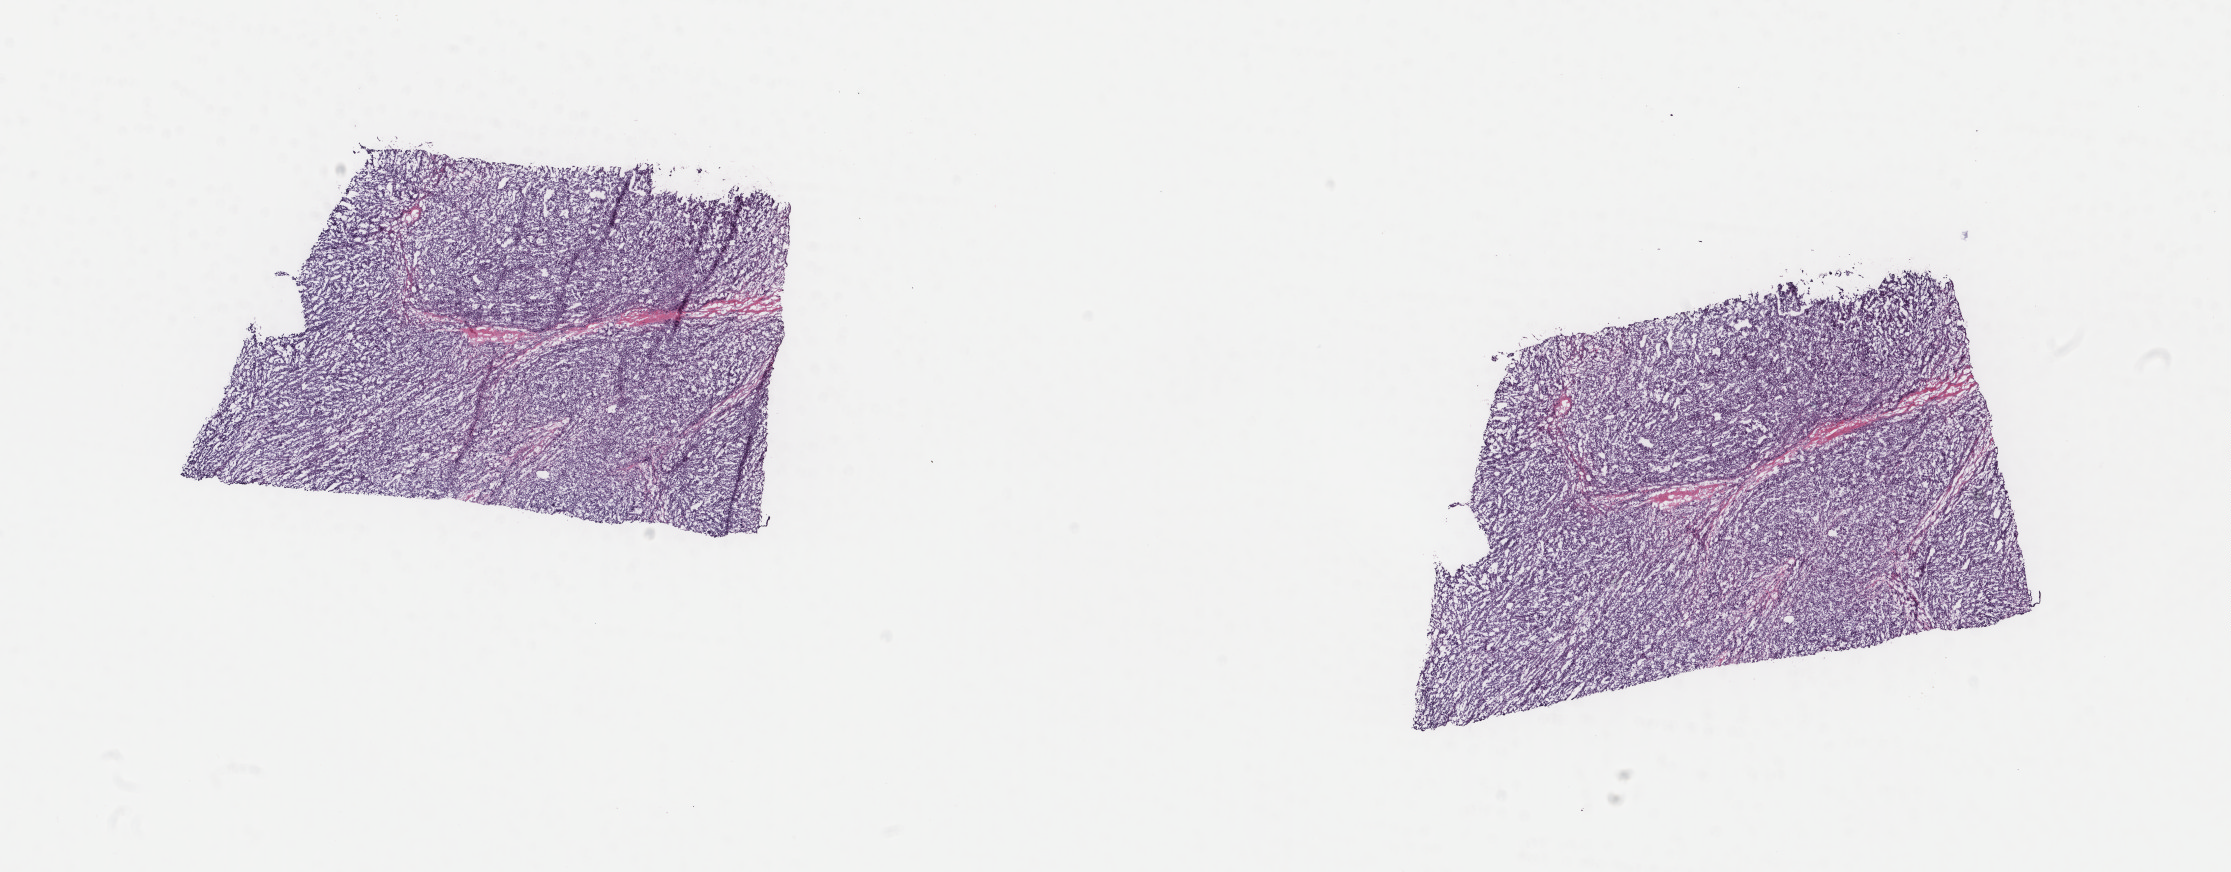
Whole-slide histology image, H&E-stained, a low-resolution overview of the entire scanned area, about 17.7 x 6.9 mm; frozen section; metastatic tumour sample, sampled site not recorded. Male patient; age at initial diagnosis 54 years. Pathologist review of this section (percent, as recorded): tumour cells 100%, tumour nuclei 97%, normal cells 0%, stromal cells 0%, necrosis 0%. Inflammatory infiltration, as recorded: lymphocyte infiltration 0%, monocyte infiltration 0%, neutrophil infiltration 0%.
• this section: metastatic tumour tissue
• patient diagnosis: Malignant melanoma, NOS